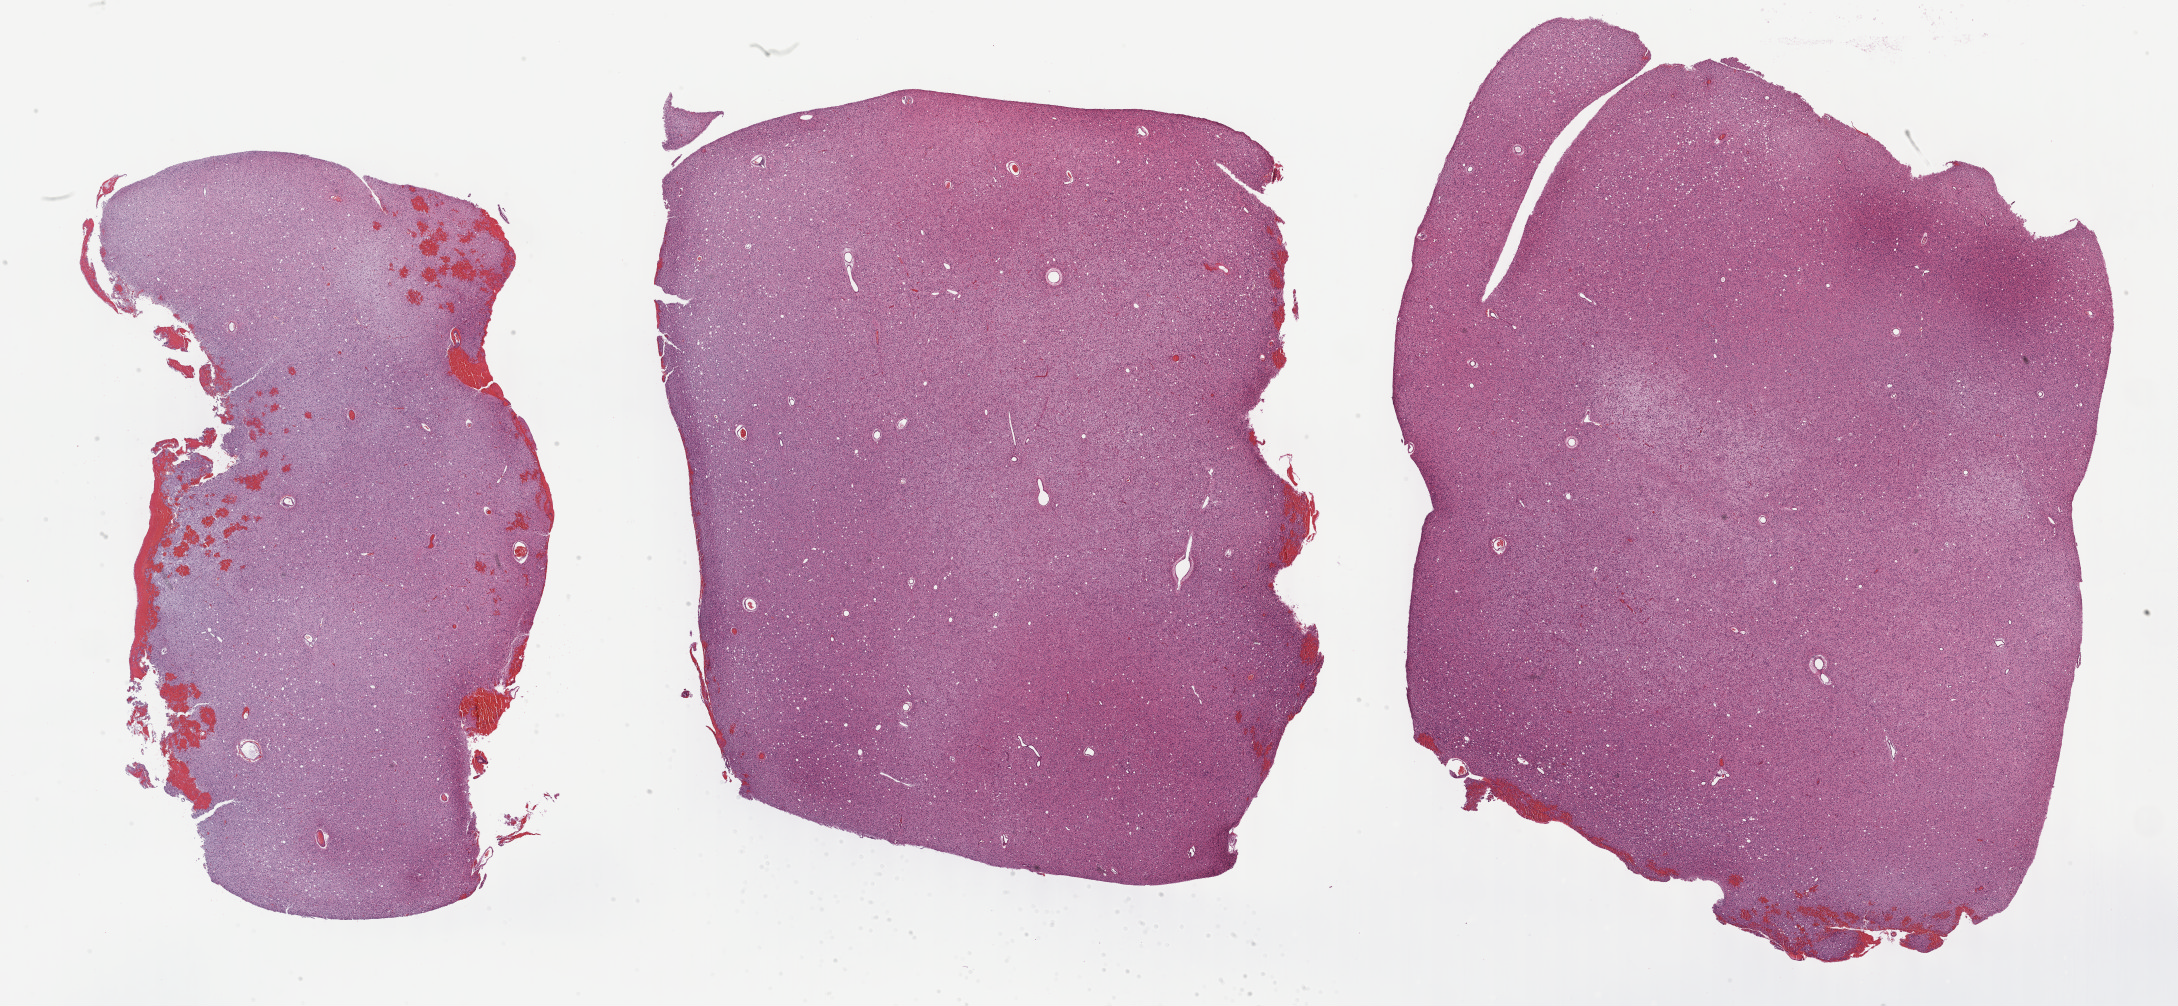
H&E-stained whole-slide image — low-resolution overview of the scanned area, about 35.2 x 16.3 mm (from a 40x scan); FFPE section; primary tumour sample from the brain. Patient: female, age at initial diagnosis 24 years. Histologic grade: G2 (moderately differentiated).
* laterality: right
* pathologic diagnosis: Astrocytoma, NOS (cerebrum)